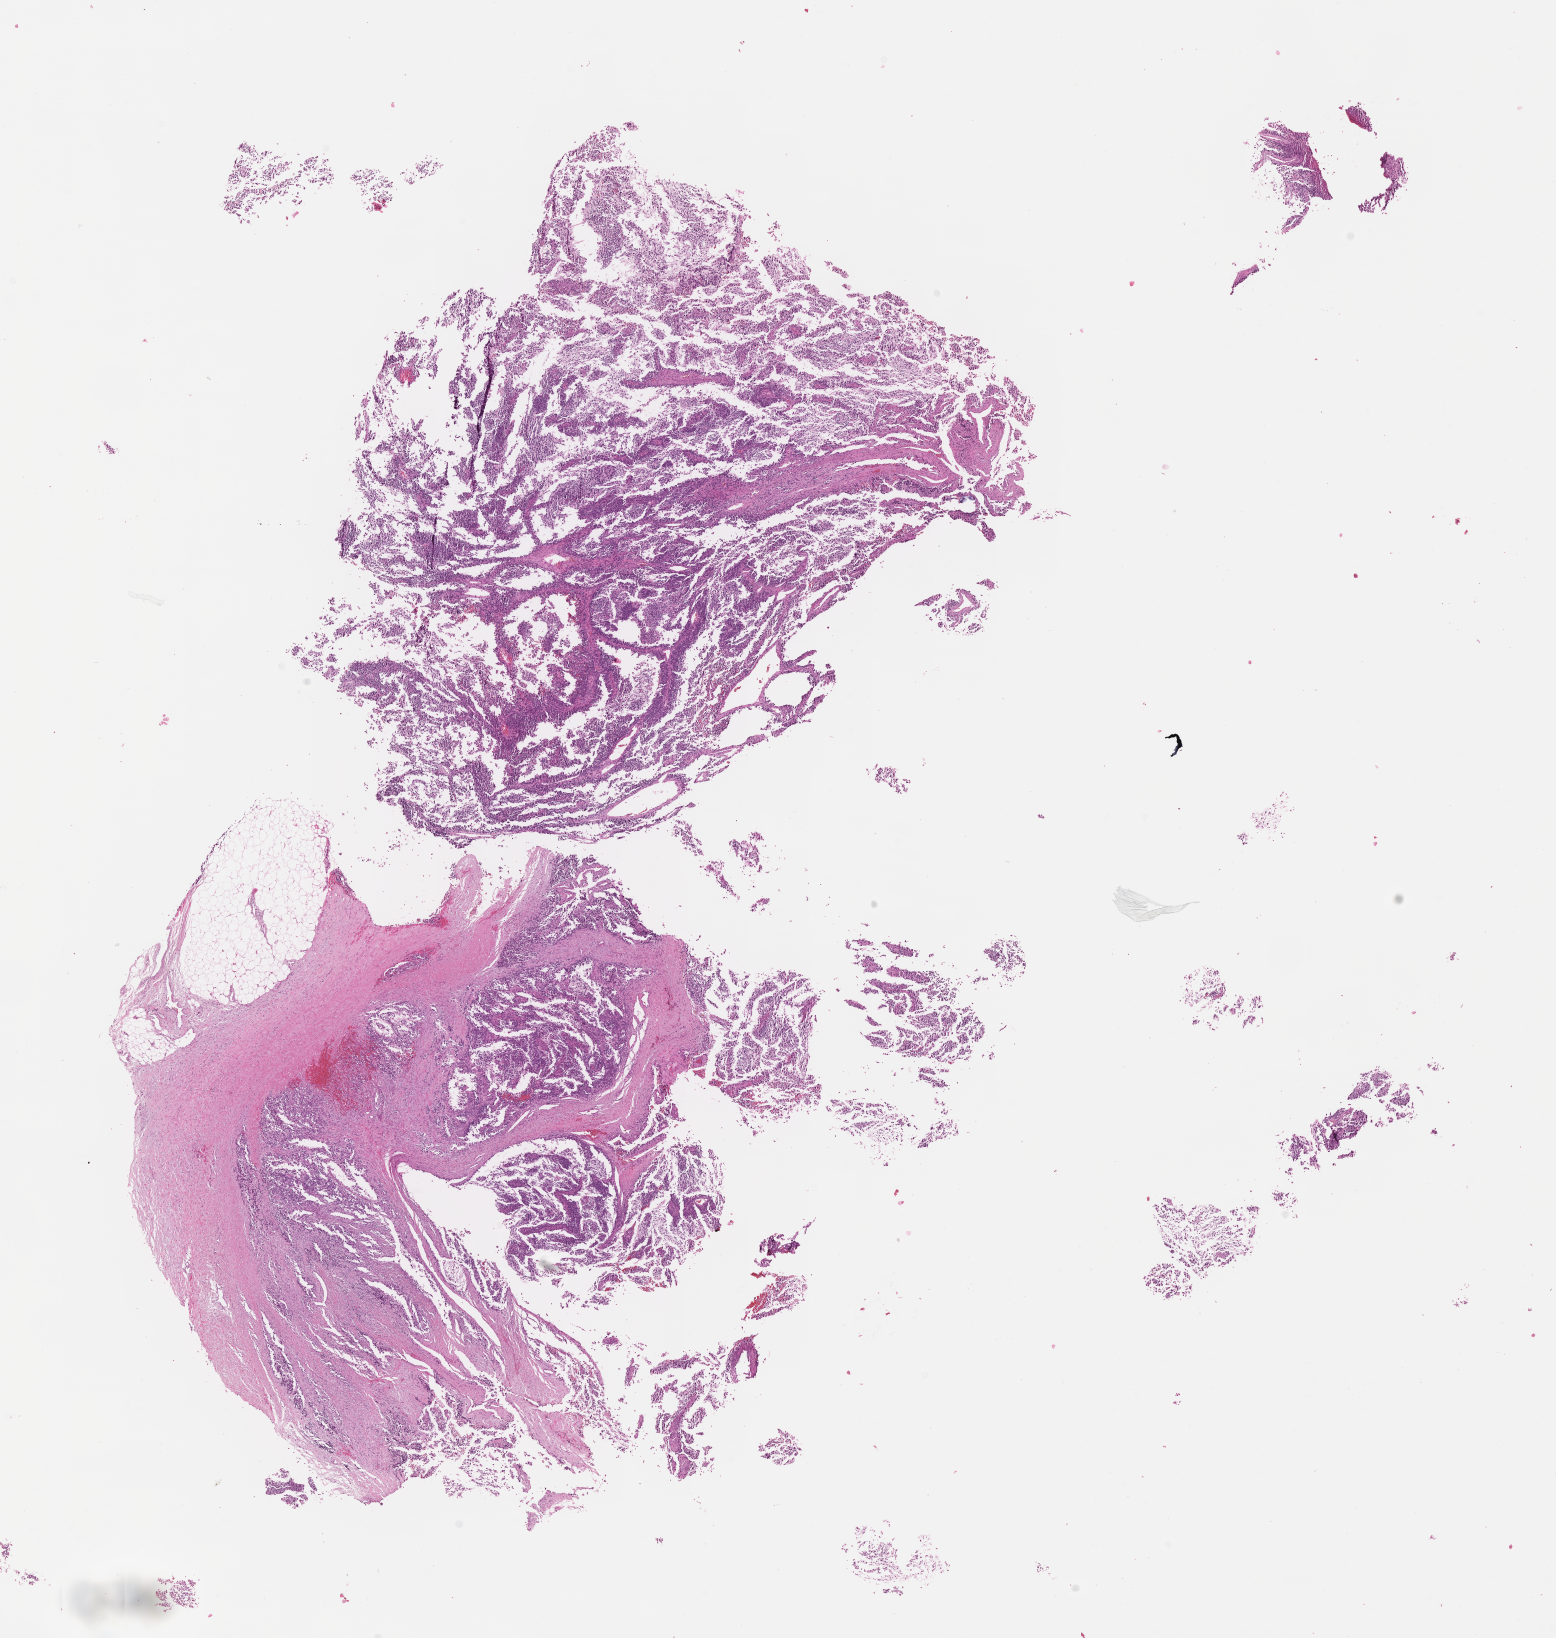
Digitized hematoxylin and eosin (H&E)-stained section of tumor tissue, shown as a low-resolution overview of the whole scanned area (about 12.6 x 13.2 mm), FFPE section, site: pelvis-left. Male patient, age at diagnosis 0.9 years.
• primary site (case record): pelvis, Site Indeterminate
• diagnosis: rhabdomyosarcoma; histological classification: embryonal rhabdomyosarcoma
• stage (as recorded): 3